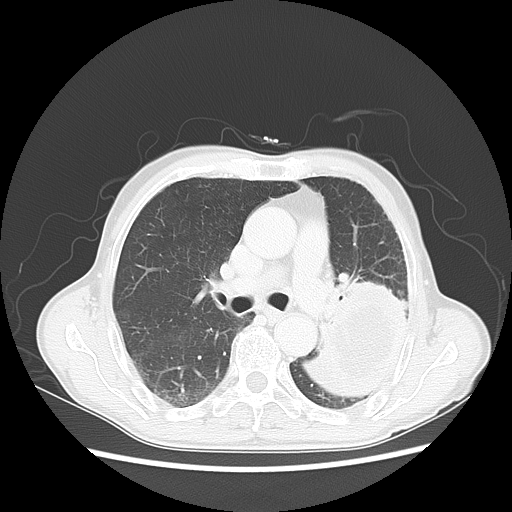
Chest CT, one axial slice; position 32 of 51 along the scan axis; 120 kVp; lung window (W 1500 / L -600 HU); 5 mm slice thickness; 512 × 512 image matrix. Patient: male, 64 years. From the clinical record (not read from this slice): clinical TNM (as recorded): T4 N0 M0; histopathological grade: G2-3.
Structures marked on this image (bounding box drawn by a radiologist):
- lung tumour (recorded histology: squamous cell carcinoma): bounding box <307,275,415,398> (left, top, right, bottom; pixels)